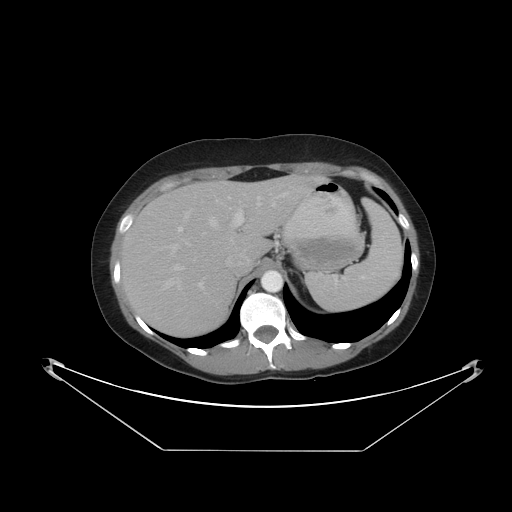
Contrast-enhanced abdominal CT, one axial slice. Reconstruction kernel STANDARD. 120 kVp. Intravenous contrast given. Soft-tissue window (W 400 / L 40 HU). 5 mm slice thickness. 512 × 512 image matrix, field of view 482 × 482 mm. Female patient, age 38 years. From the clinical record (not read from this slice): diagnosis: colorectal cancer liver metastases, imaged before liver resection; multiple liver metastases: yes; largest metastasis: 2.5 cm; disease in both lobes: no.
Outlined on this slice (outlined manually by an expert reader):
- hepatic veins: bounding box <165,193,257,288> (left, top, right, bottom; pixels)
- liver: <120,176,322,337>
- planned liver remnant (the part of the liver to remain after resection): <181,176,306,256>
- portal vein (with intrahepatic branches): <178,192,289,287>
- liver metastasis: <305,178,317,190>